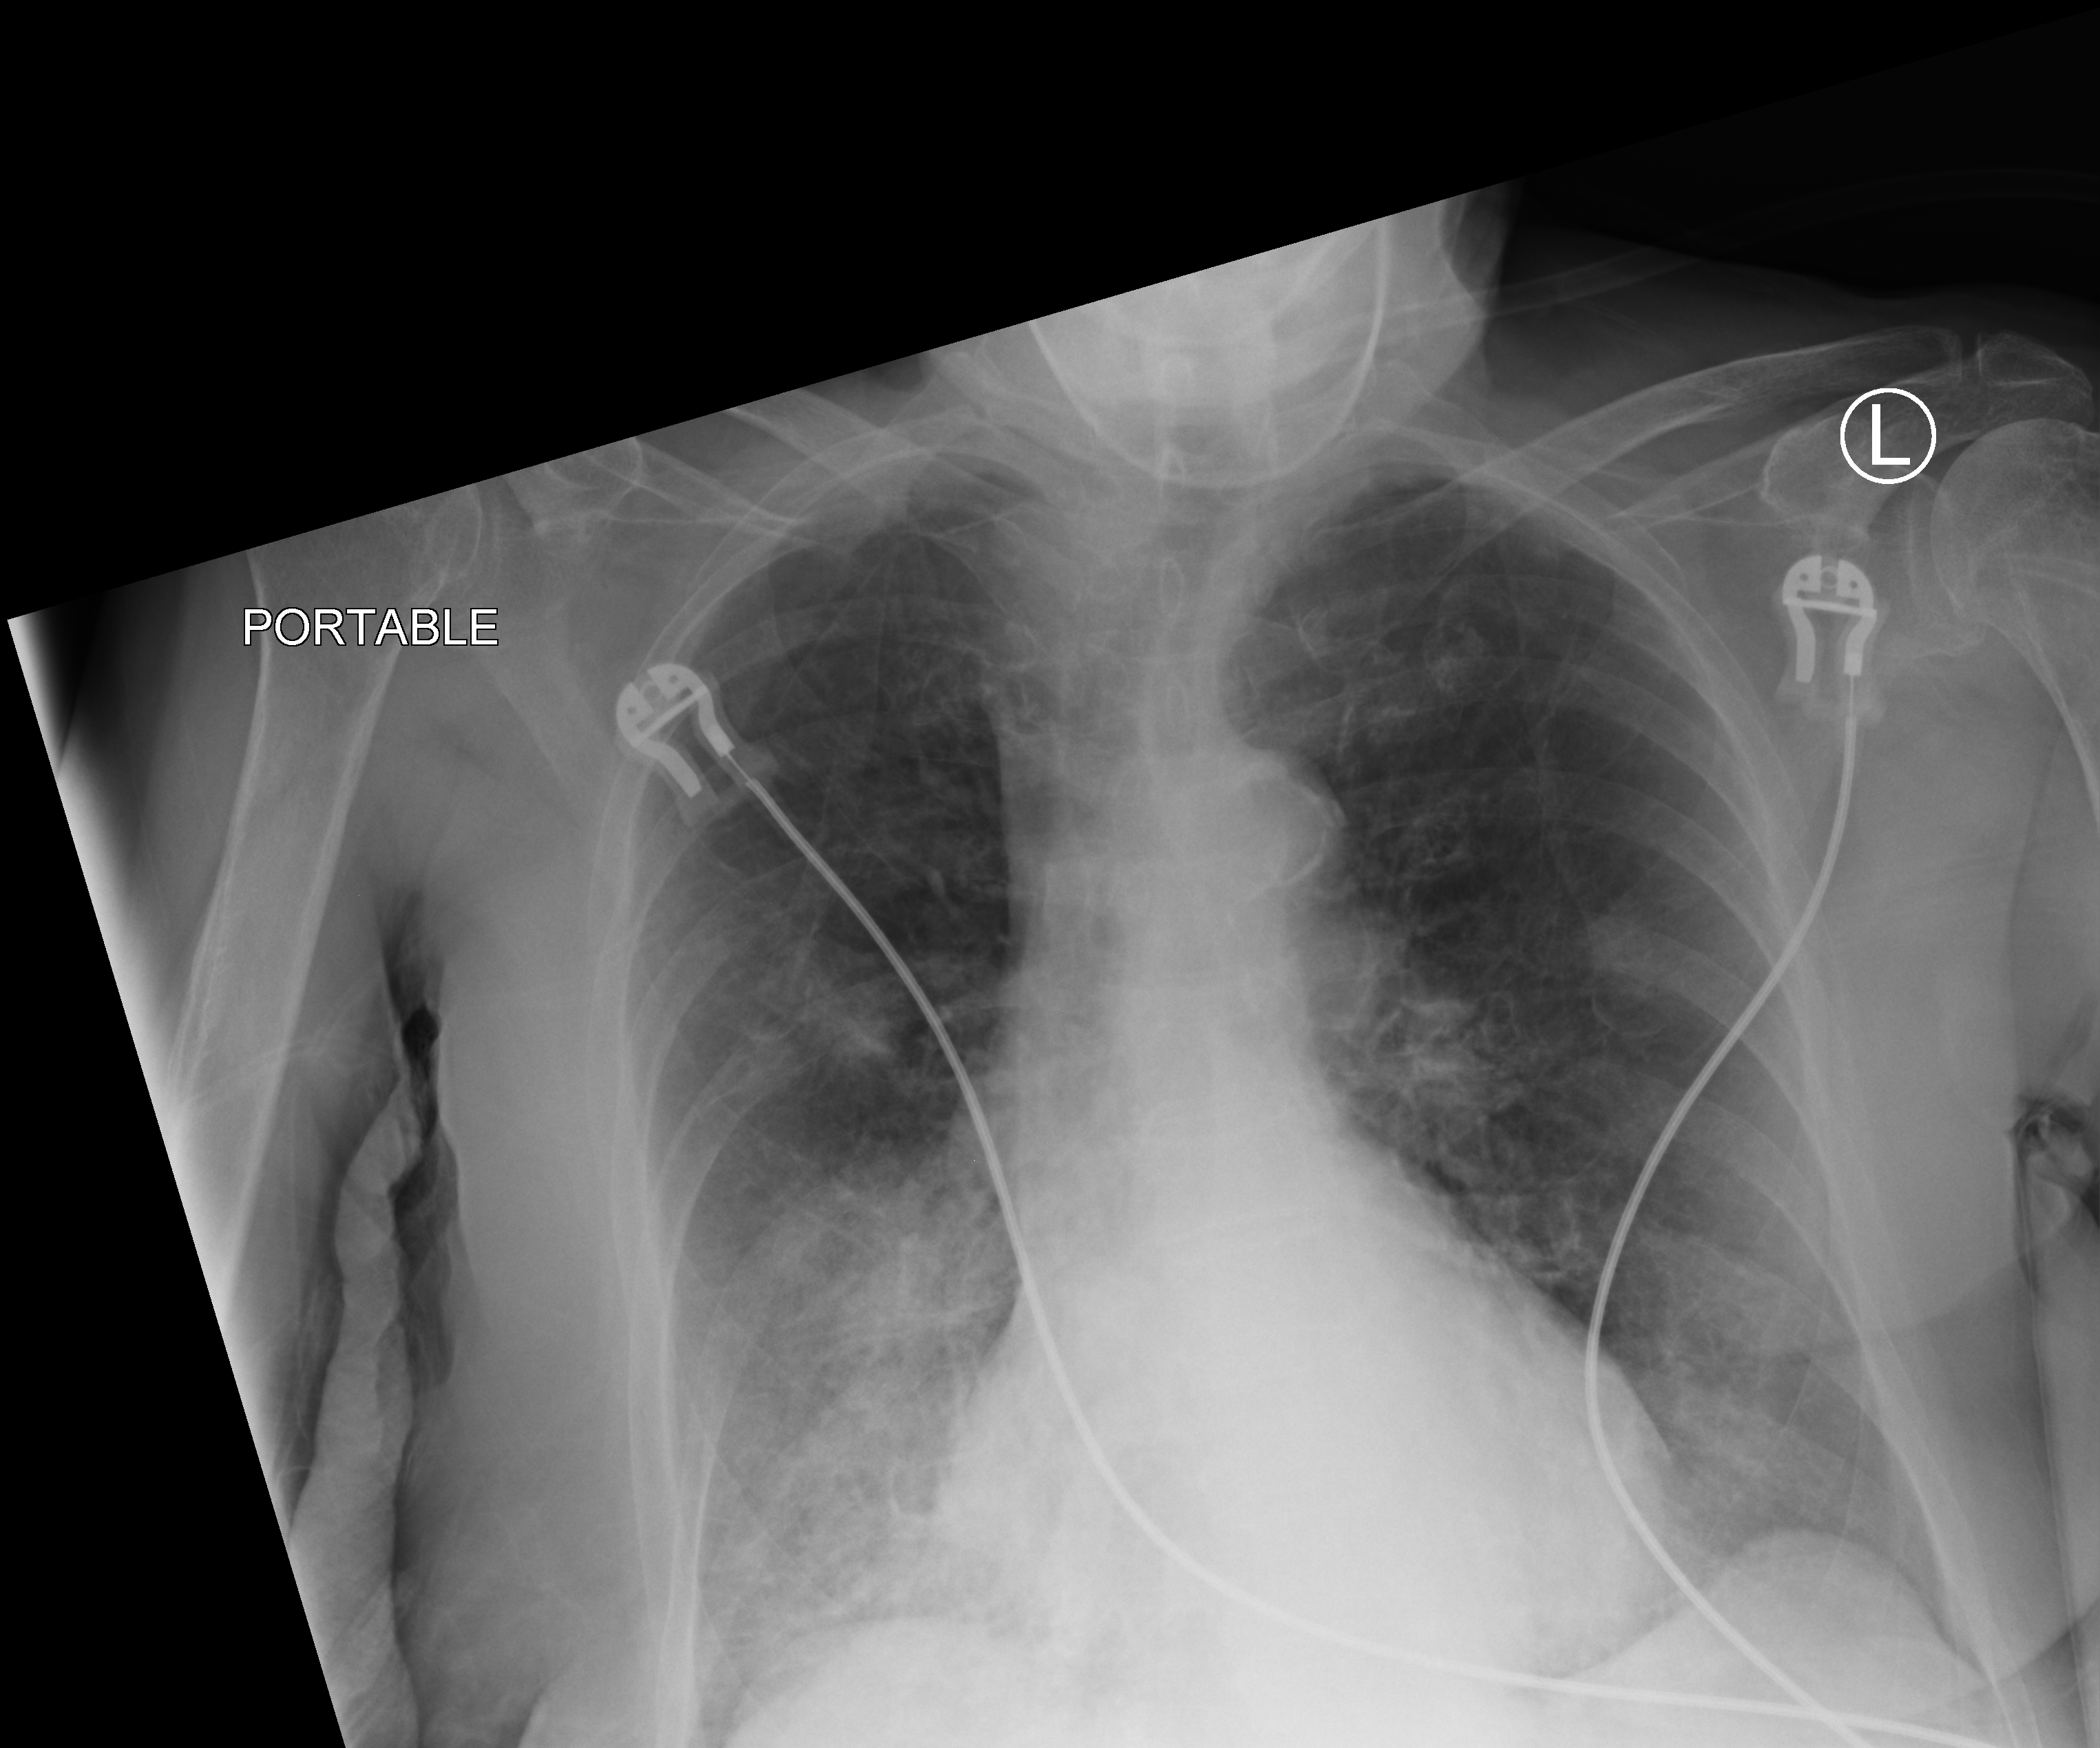
Portable chest radiograph. Female patient hospitalised with COVID-19, age 75–90 years.
From the hospital-stay record, not from the radiograph (when in the stay this image was taken is not recorded): admitted to intensive care during this hospital stay: no; mechanically ventilated during this hospital stay: no.